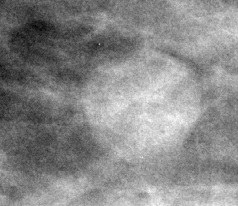
Cropped region of a digitized screen-film mammogram centred on a radiologist-marked abnormality; right breast; MLO view; BI-RADS breast density category 1 (scale 1–4).
Mass, shape round, margins circumscribed; BI-RADS assessment category 3; subtlety rating 5 on a 1 (subtle) to 5 (obvious) scale; benign without callback (not worked up further).